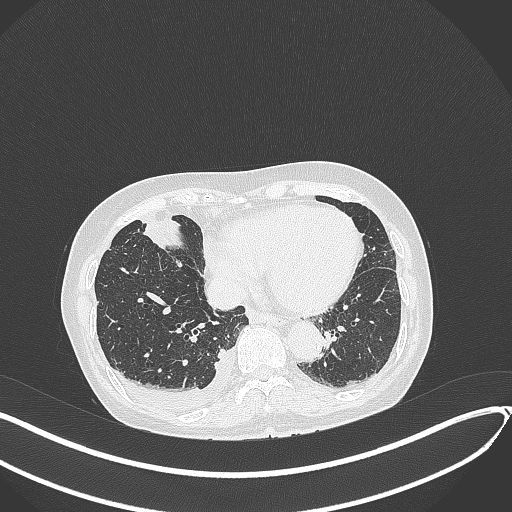
Chest CT, one axial slice. Slice 116 of 418 in the series (ordered by position). Reconstruction kernel B70f. Lung window (W 1500 / L -600 HU). 1 mm slice thickness. 512 × 512 image matrix, field of view 400 × 400 mm. Female patient, age 75 years. Case-level facts recorded for this patient, not image findings: clinical TNM (as recorded): T2a N3 M0.
Structures marked on this image (bounding box drawn by a radiologist):
- lung tumour (recorded histology: adenocarcinoma): box from (x=143, y=216) to (x=195, y=253) px